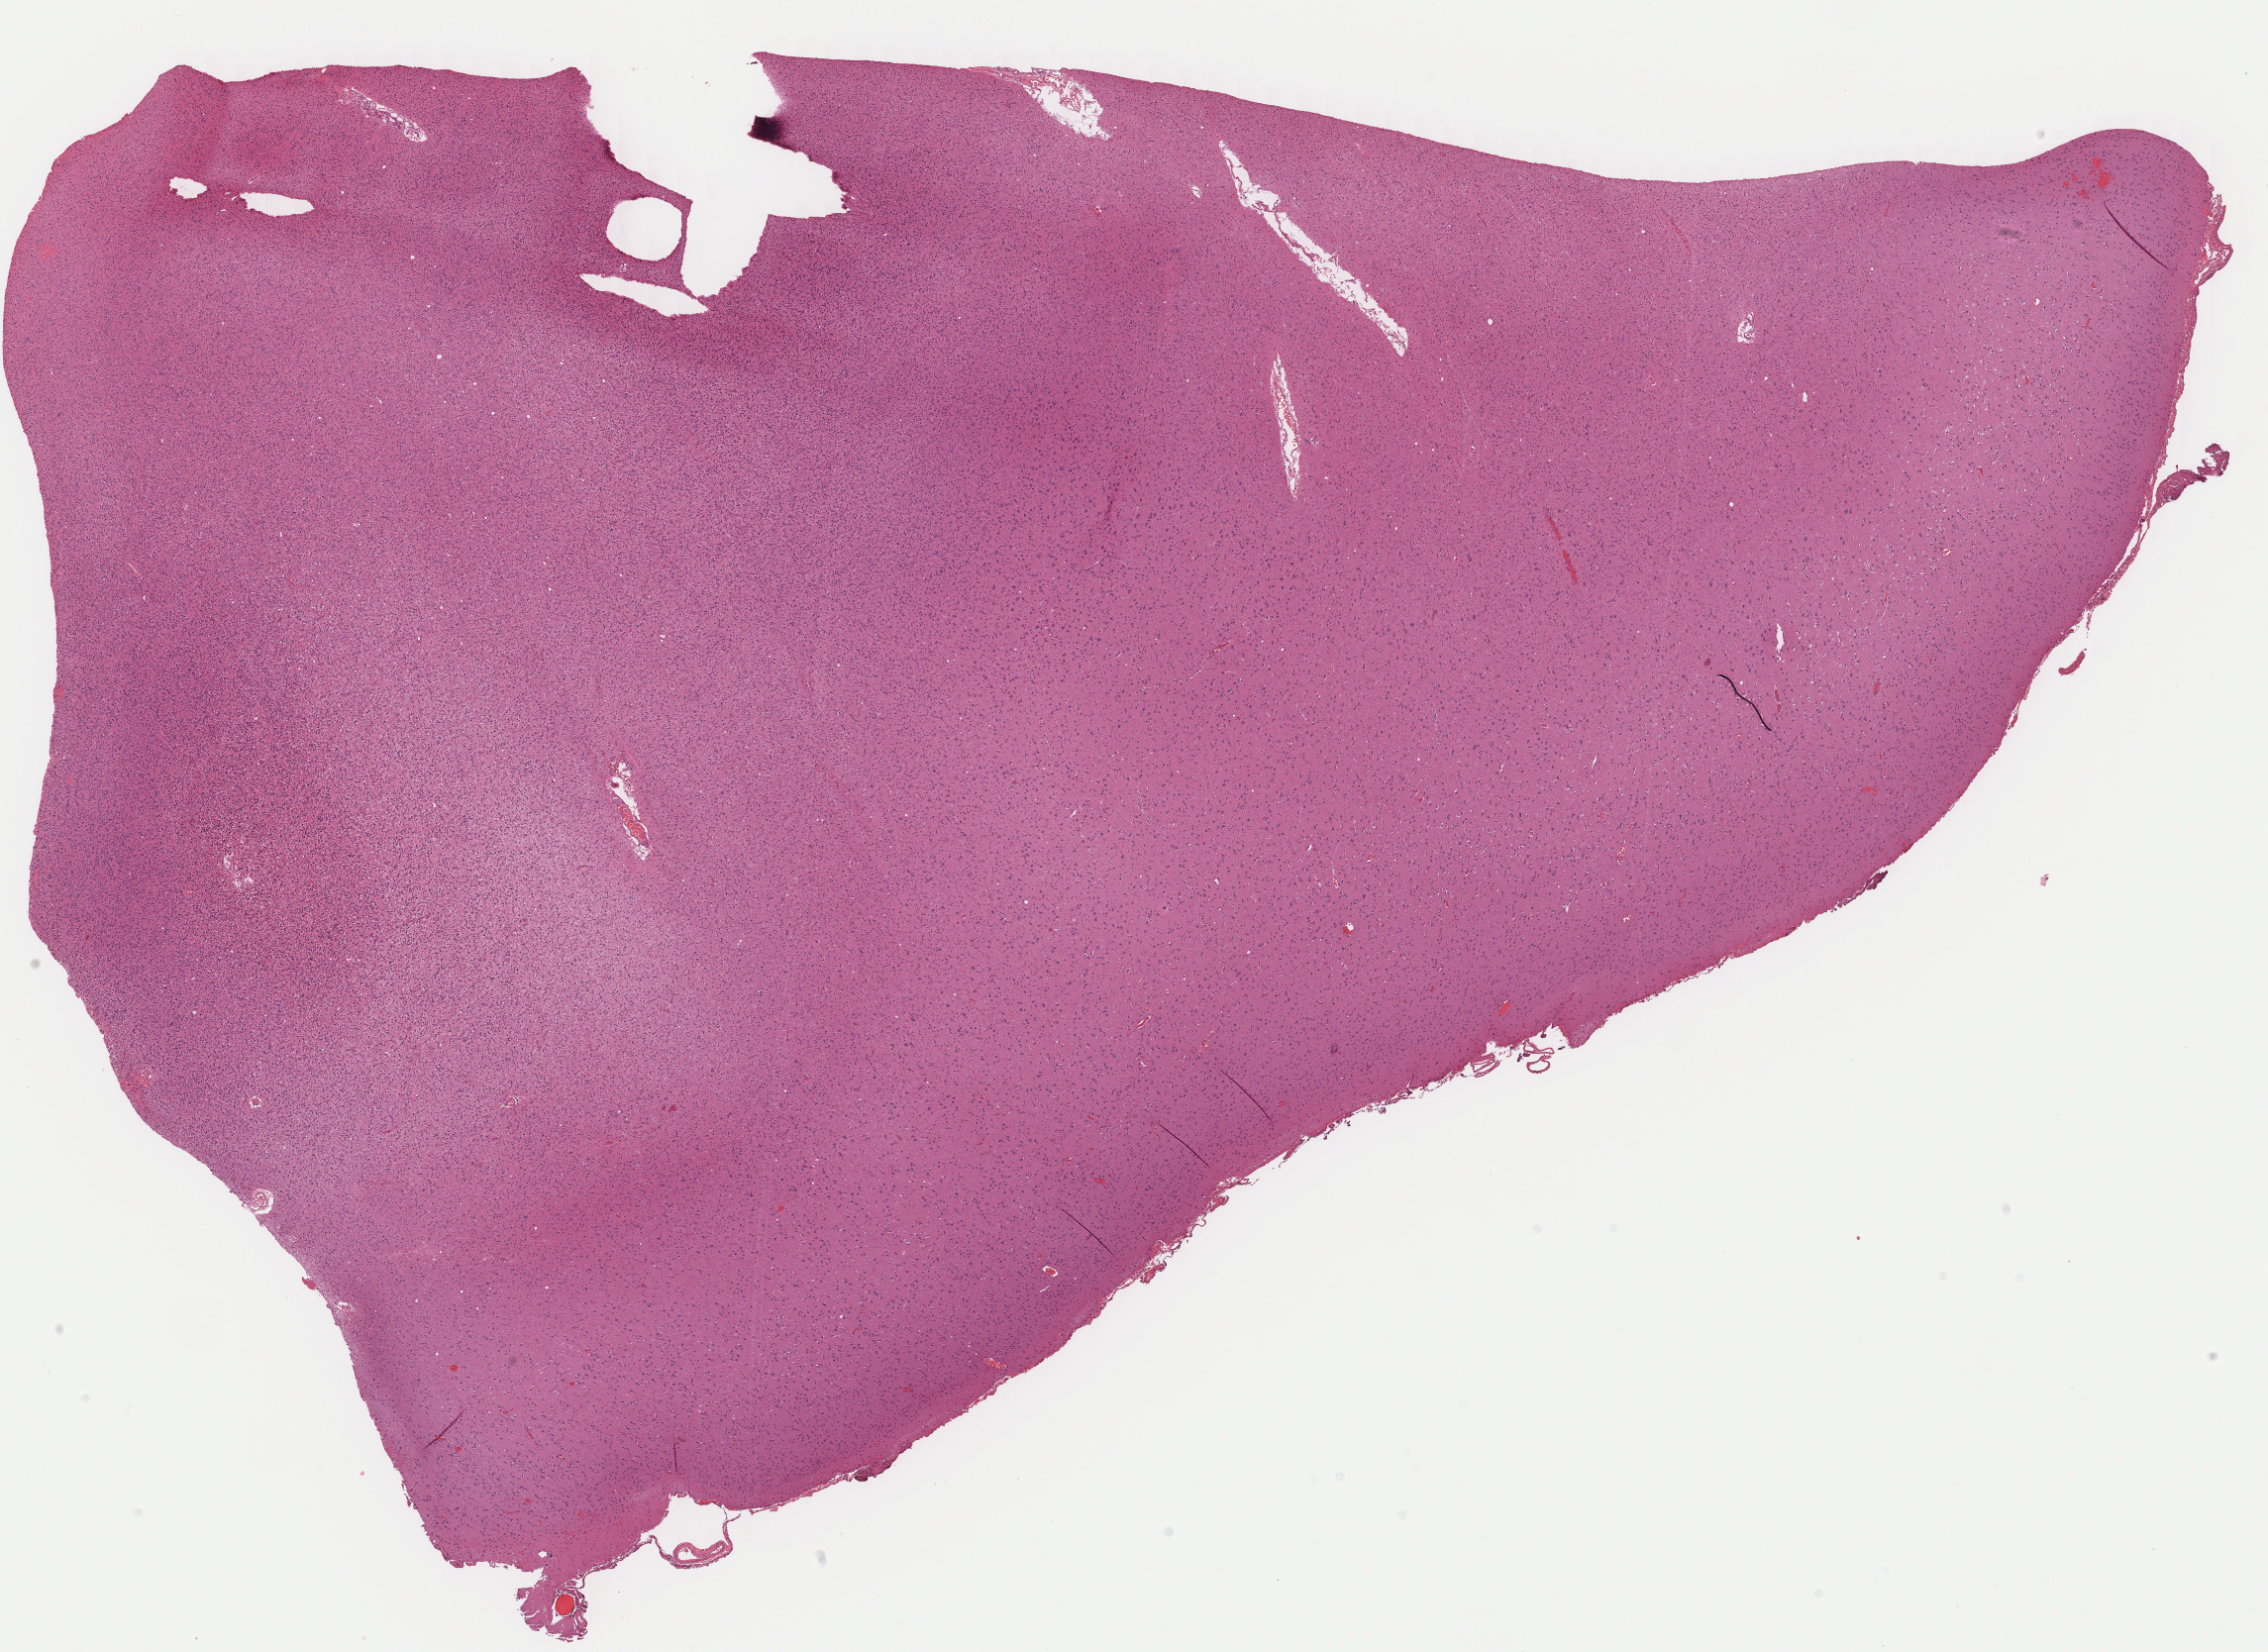
Digitized Hematoxylin and eosin (H&E) stained tissue section (whole slide) — a low-resolution overview of the entire scanned area, about 18.0 x 13.1 mm. Formalin-fixed paraffin-embedded (FFPE) diagnostic section. Brain, primary tumour sample. Patient: male, age at initial diagnosis 43 years. Histologic grade: G2 (moderately differentiated).
* pathologic diagnosis: Mixed glioma (cerebrum)
* laterality: right